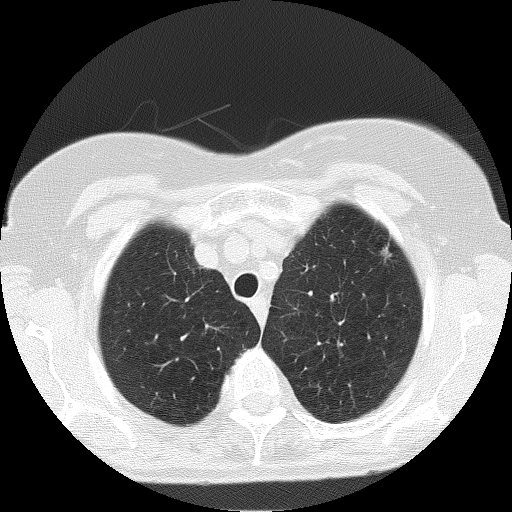
Low-dose screening chest CT, one axial slice; slice 141 of 166 in the series (ordered by position); reconstruction kernel FC51; 120 kVp; lung window (W 1500 / L -600 HU); 512 × 512 image matrix.
Structures marked on this image (expert manual segmentation):
- lesion 4 (nodule, upper lobe of left lung): bounding box (x1, y1, x2, y2) in pixels: (380, 247, 391, 260)